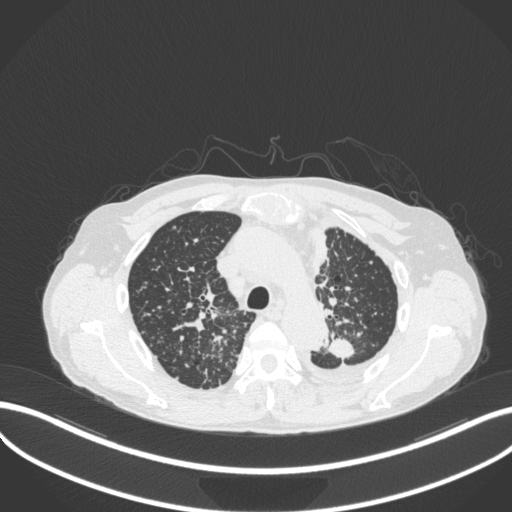
Chest CT, one axial slice. Position 262 of 319 along the scan axis. Reconstruction kernel B31f. 120 kVp. Lung window (W 1500 / L -600 HU). 1 mm slice thickness. 512 × 512 image matrix. Patient: male, 58 years. From the clinical record (not read from this slice): clinical TNM (as recorded): T1c N3 M1.
Outlined on this slice (rectangle marked by the reading radiologist):
- lung tumour (recorded histology: adenocarcinoma): box from (x=326, y=332) to (x=355, y=361) px